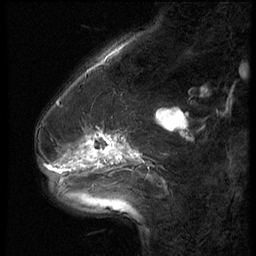
Breast MRI (dynamic contrast-enhanced), one sagittal slice. 3 images stored at this slice position (order not interpretable as contrast timing). 1.5 T. TE 4.2 ms, TR 9 ms. 256 × 256 image matrix, field of view 180 × 180 mm. Female patient, age 54 years. From the clinical record (not read from this slice): setting: breast cancer imaged before/during neoadjuvant chemotherapy; receptor status: HR-positive, HER2-negative.
Outlined on this slice (semi-automatic segmentation, software-assisted and operator-edited):
- analysis volume of interest (the breast-tissue region the enhancement analysis was run in; not a lesion): box from (x=42, y=126) to (x=146, y=183) px
- tumour enhancement mask (voxels above the 140 % enhancement threshold inside the analysis volume of interest): (x=89, y=135)–(x=121, y=160)